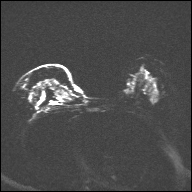
Breast MRI, one axial slice; diffusion-weighted series; image 2 of 4 stored at this slice position (different b-values; order by instance number); 1.5 T; 192 × 192 image matrix, field of view 360 × 360 mm. Female patient.
Structures marked on this image (expert manual segmentation):
- tumour on diffusion-weighted imaging: box from (x=38, y=79) to (x=59, y=90) px